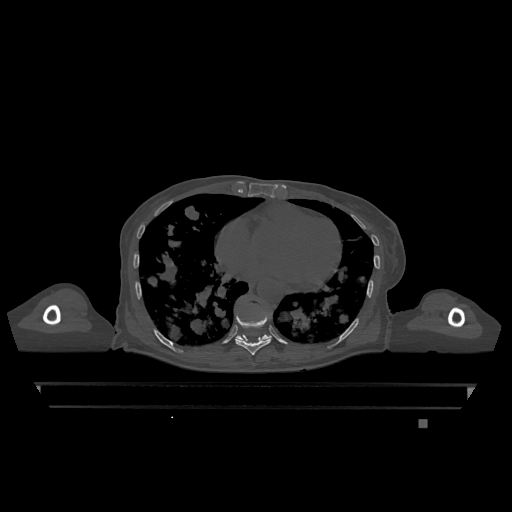
CT including the spine, one axial slice. Position 678 of 1317 along the scan axis. Bone window (W 1800 / L 400 HU). 0.5 mm slice thickness. 512 × 512 image matrix. Female patient, age 74 years. From the clinical record (not read from this slice): primary cancer: lung; vertebrae with lytic lesions (as recorded): T1, T4, T5, T6, L4, L5.
Annotated regions visible in this slice (semi-automatic segmentation, software-assisted and operator-edited):
- T10 vertebra: box from (x=236, y=335) to (x=272, y=340) px
- T9 vertebra: (x=235, y=307)–(x=271, y=355)